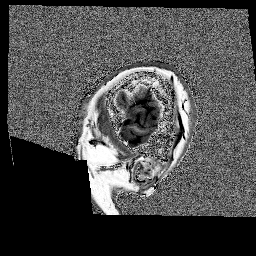
Brain MRI from a brain-tumour surgery series, one sagittal slice; slice 24 of 176 in the series (ordered by position); 1 mm slice thickness; 256 × 256 image matrix. Case-level facts recorded for this patient, not image findings: histopathology: Glioblastoma; WHO grade: 4; IDH mutation: no.
Annotated regions visible in this slice (expert manual segmentation):
- tumour: bounding box <144,91,150,96> (left, top, right, bottom; pixels)